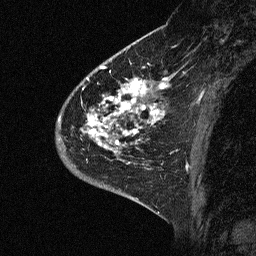
Breast MRI (dynamic contrast-enhanced), one sagittal slice; slice 19 of 64 in the series (ordered by position); dynamic contrast-enhanced study with each time point stored as its own series, time point 2 of 3 at this slice position (early post-contrast, ordered by acquisition time); 1.5 T; TE 4.5 ms, TR 11 ms; 2.06 mm slice thickness; 256 × 256 image matrix. Patient: female, 46 years. From the clinical record (not read from this slice): setting: breast cancer imaged before/during neoadjuvant chemotherapy; receptor status: HER2-positive.
Outlined on this slice (semi-automatic segmentation, software-assisted and operator-edited):
- analysis volume of interest (the breast-tissue region the enhancement analysis was run in; not a lesion): bounding box [x1, y1, x2, y2] px = [44, 72, 176, 177]
- tumour enhancement mask (voxels above the 90 % enhancement threshold inside the analysis volume of interest): [80, 72, 166, 164]